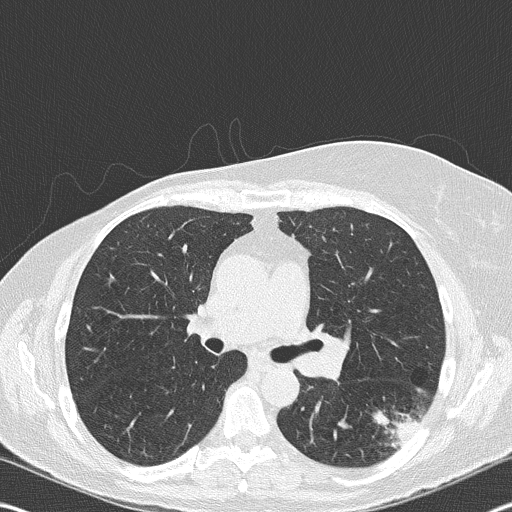
Axial slice from a low-dose chest CT screening exam; second screening round (one year after baseline); lung window (W 1500 / L -600 HU); 2 mm slice thickness; lung (sharp) reconstruction kernel (B50f); 120 kVp. Female participant, aged 60 years at enrolment. Current smoker at enrolment.
Lesion marked by an expert reader, bounding box (x1, y1, x2, y2) in pixels: (370, 385, 438, 451). The exam's reader record, not a measurement of the box and not confirmed to be the same lesion: non-calcified nodule or mass ≥4 mm, left lower lobe, 18 × 16 mm, spiculated (stellate) margins, soft tissue attenuation, pre-existing on the prior screen: no. Lung cancer was diagnosed 35 days after this screen: carcinoma, NOS, left hilum, stage IV (AJCC 6th edition), 45 mm at pathology.